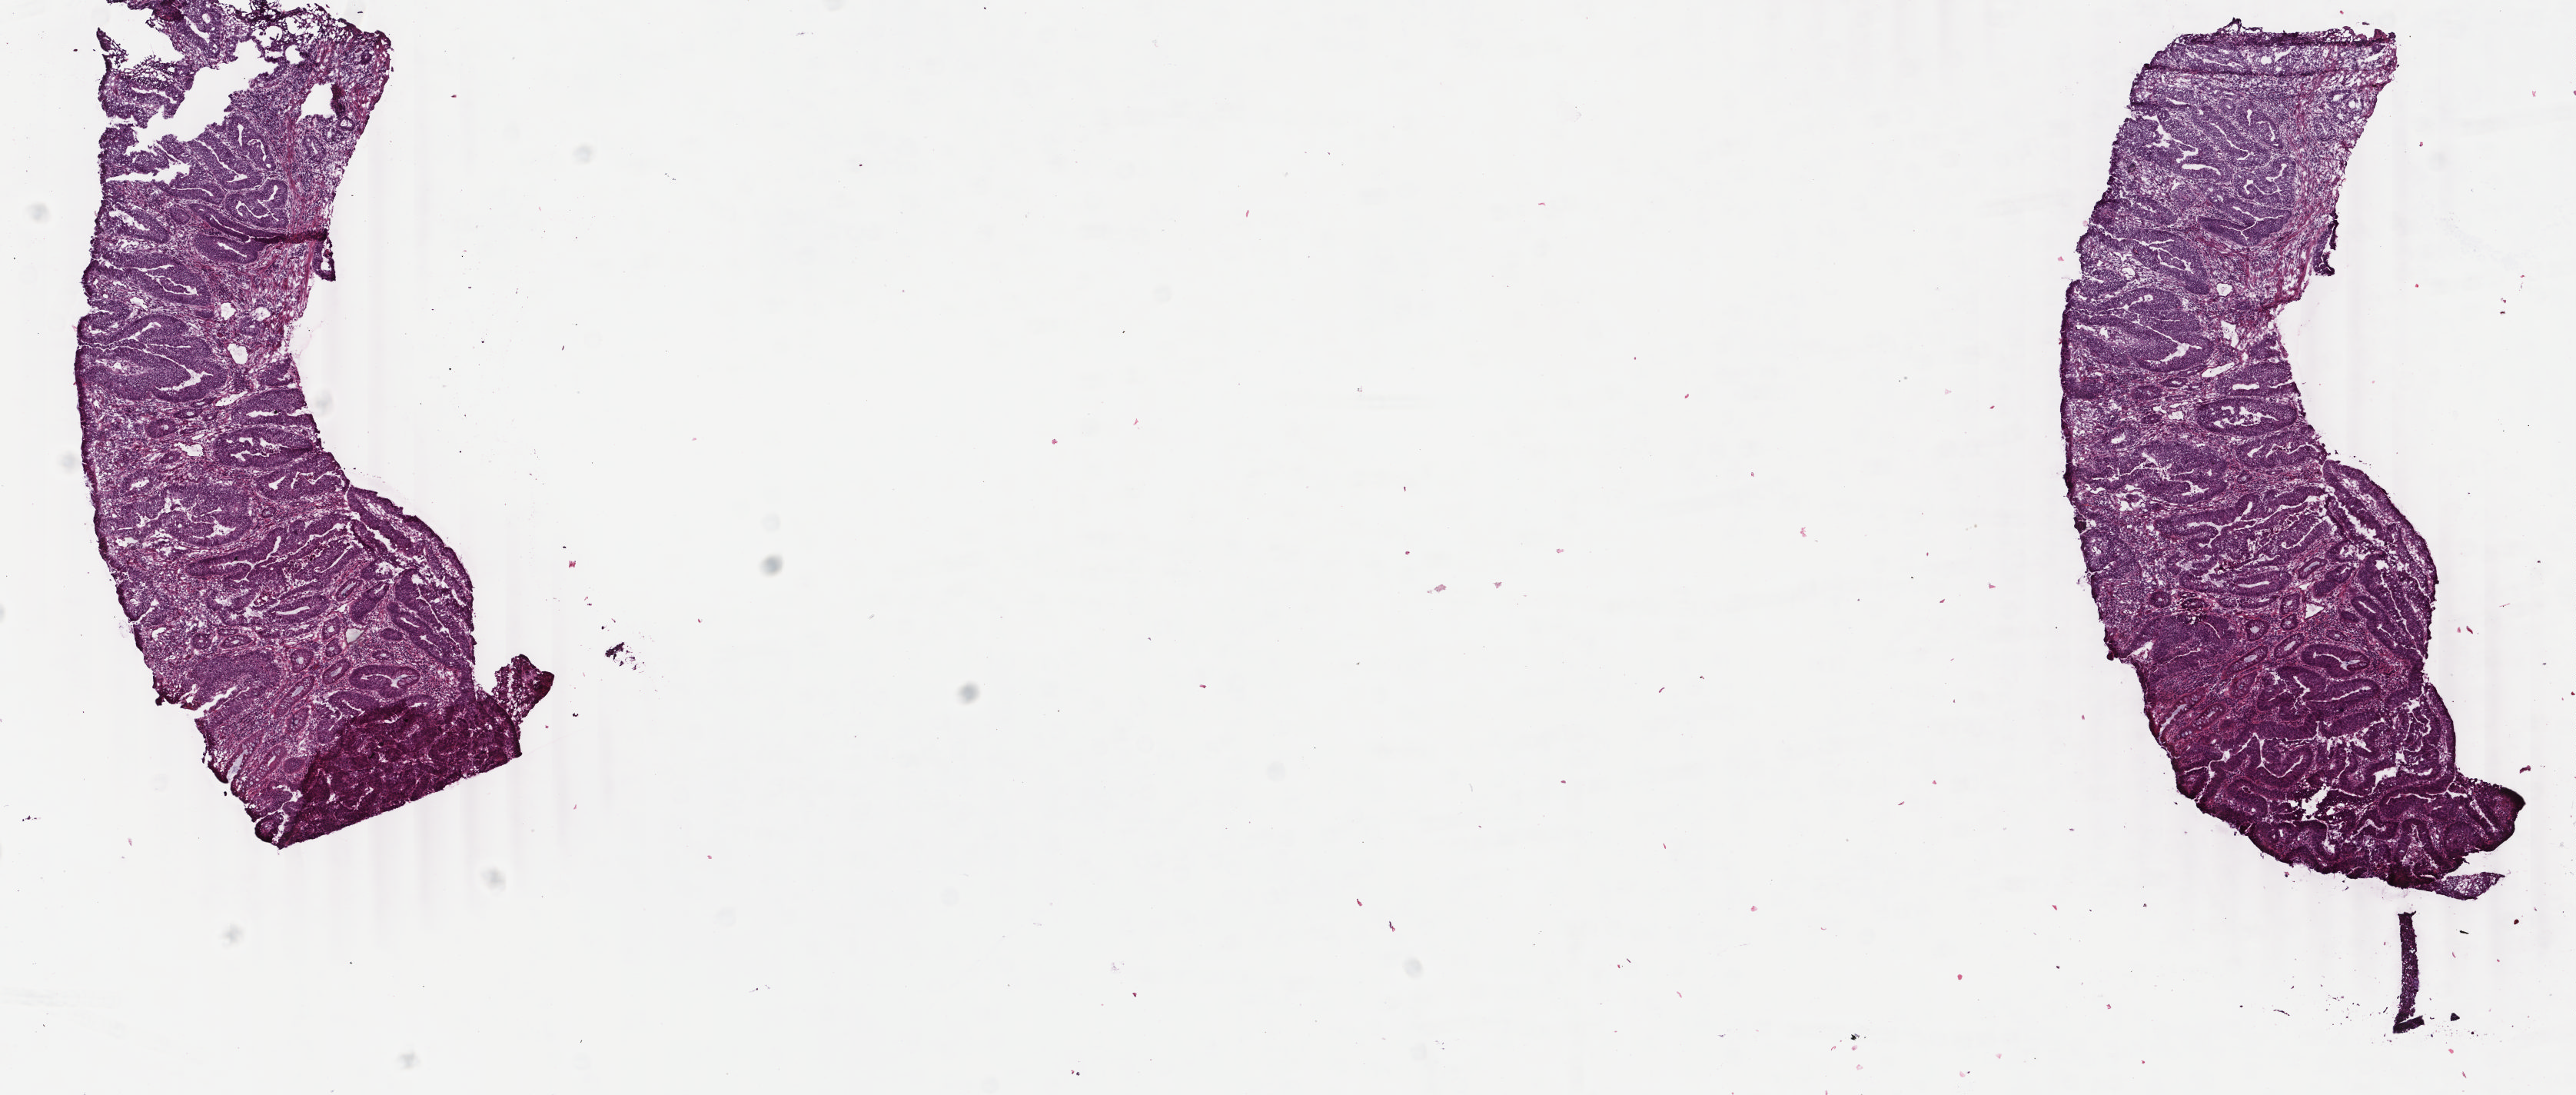
Whole-slide histology image, H&E — whole scanned area (about 13.3 x 5.7 mm, acquisition: 40x scan) shown as a low-resolution overview, frozen section from the top of the tissue portion, primary tumour sample from the colon. Patient: male, age at initial diagnosis 70 years. Slide review estimates, as recorded: tumour cells 90%, tumour nuclei 80%, normal cells 0%, stromal cells 4%, necrosis 1%. Inflammatory infiltration, as recorded: lymphocyte infiltration 10%, monocyte infiltration 1%, neutrophil infiltration 2%.
AJCC pathologic stage: IIA (6th edition). Histologic diagnosis: Adenocarcinoma, NOS (sigmoid colon).